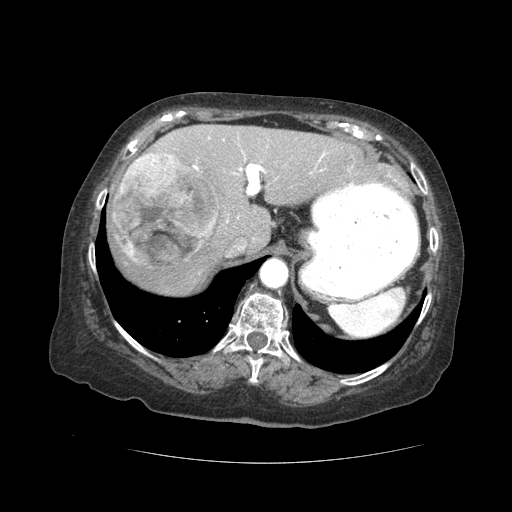
Contrast-enhanced abdominal CT (liver protocol), one axial slice; slice 32 of 59 in the series (ordered by position); reconstruction kernel STANDARD; 120 kVp; soft-tissue window (W 400 / L 40 HU); 512 × 512 image matrix. From the clinical record (not read from this slice): diagnosis: hepatocellular carcinoma (patient treated with transarterial chemoembolisation; whether this scan precedes or follows treatment is not stated here); TNM stage (as recorded): Stage-I; Child-Pugh class: A; tumour nodularity: uninodular.
Annotated regions visible in this slice (semi-automatic segmentation, software-assisted and operator-edited):
- abdominal aorta: bounding box [x1, y1, x2, y2] px = [261, 260, 287, 289]
- liver parenchyma outside the tumour (the mass and vessels are separate outlines, so this box may not span the whole liver): [108, 124, 376, 294]
- mass: [113, 152, 218, 271]
- liver vessels: [193, 137, 353, 223]